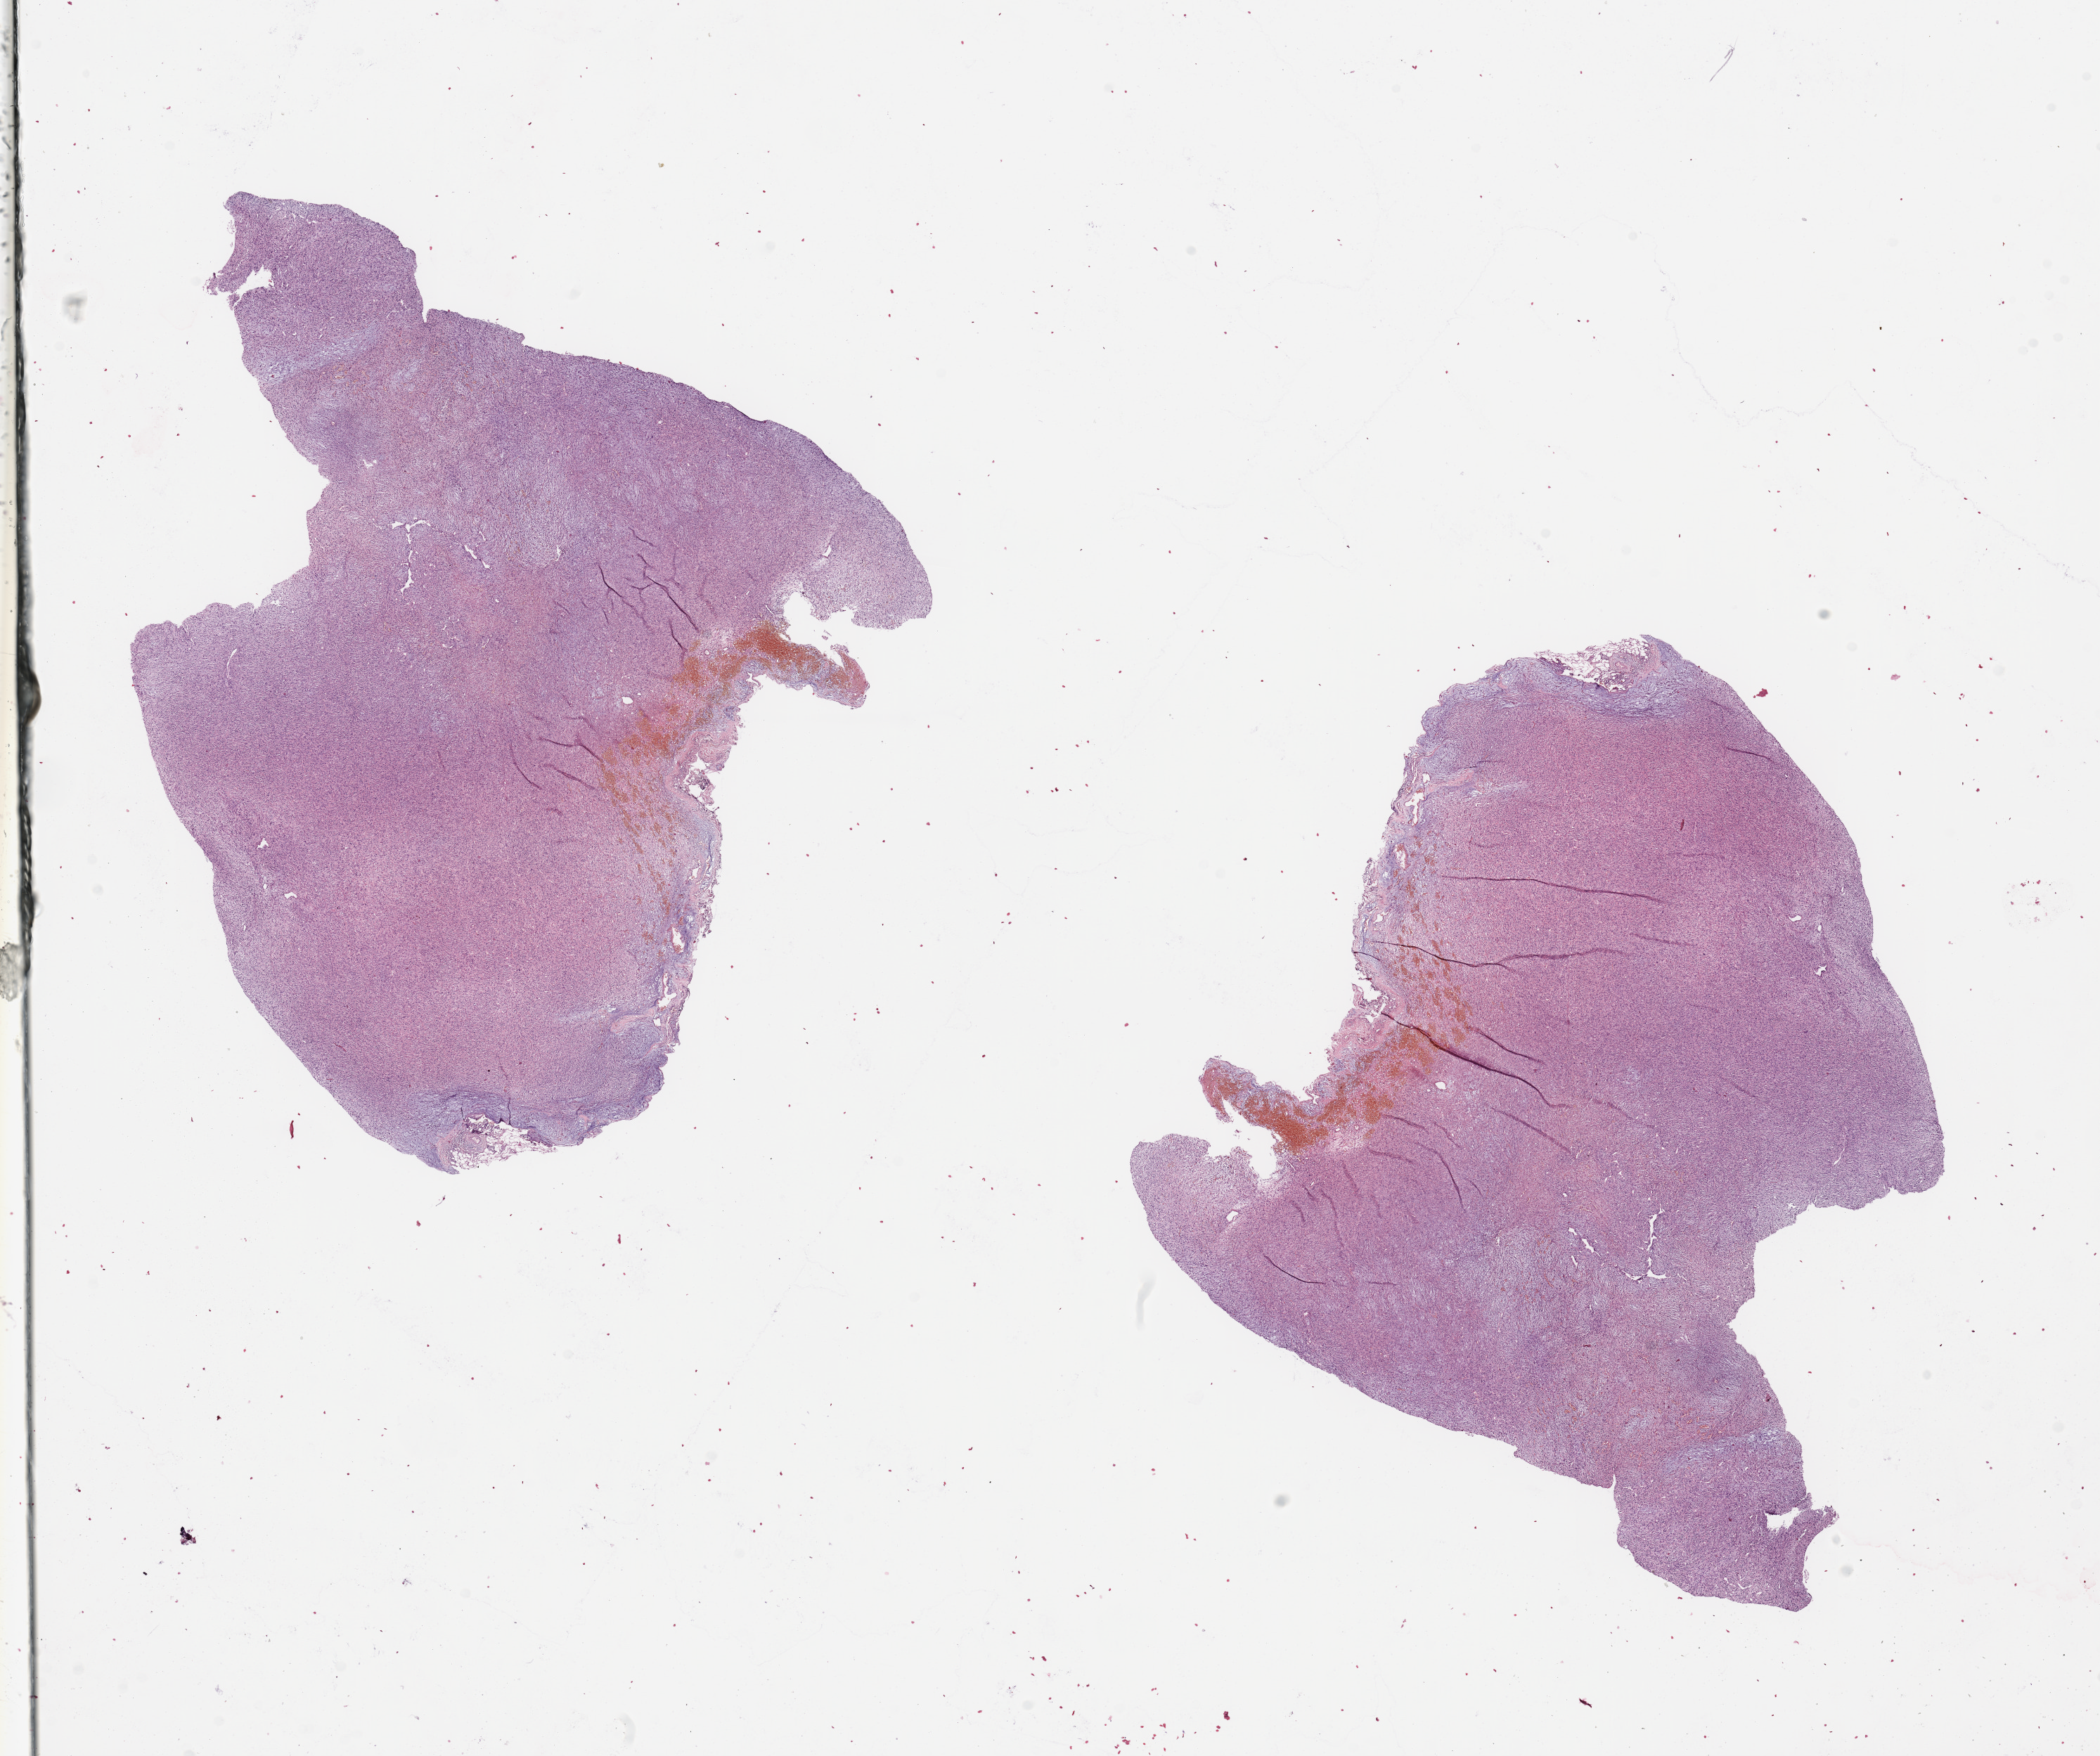
Whole-slide histology image, Hematoxylin and eosin (H&E) stained, shown as a low-resolution overview of the whole scanned area (about 23.6 x 19.8 mm, slide scanned at 20x). Tumour tissue sample. Patient: female, age 72 years.
Primary tumour site (as recorded): superficial trunk. Patient diagnosis (cohort enrolment): sarcoma (site not recorded at cohort level).